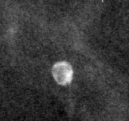
Region of interest cut from a scanned film mammogram (one marked finding); left breast; MLO view.
- Marked abnormality: calcifications, morphology lucent centered; BI-RADS assessment category 2; subtlety rating 3 on a 1 (subtle) to 5 (obvious) scale; benign without callback (not worked up further).